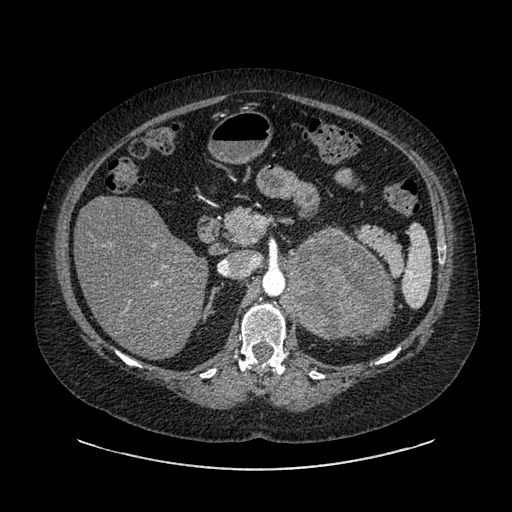
Contrast-enhanced abdominal CT, one axial slice; slice 561 of 769 in the series (ordered by position); reconstruction kernel SOFT; intravenous contrast given; soft-tissue window (W 400 / L 40 HU); 0.62 mm slice thickness; 512 × 512 image matrix, field of view 460 × 460 mm. Female patient, age 61 years. Case-level facts recorded for this patient, not image findings: diagnosis: adrenocortical carcinoma; tumour side: left adrenal; tumour size at pathology: 13 cm; Ki-67 index: 79 %; stage (as recorded): 2.
Outlined on this slice (semi-automatic segmentation, software-assisted and operator-edited):
- mass: bounding box (x1, y1, x2, y2) in pixels: (282, 229, 391, 341)